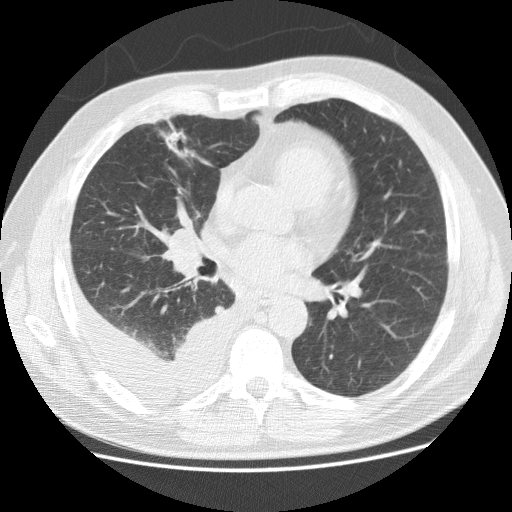
Axial slice from a low-dose chest CT screening exam; baseline screening round; lung window (W 1500 / L -600 HU); 2.5 mm slice thickness; 120 kVp. Male, age 65 years at enrolment. Current smoker at enrolment.
Expert-annotated lung lesion, bounding box (x1, y1, x2, y2) in pixels: (149, 121, 215, 174). The exam's reader record, not a measurement of the box and not confirmed to be the same lesion: non-calcified nodule or mass ≥4 mm, right middle lobe, 22 × 15 mm, spiculated (stellate) margins, mixed attenuation. Official screen result: positive, change unspecified: nodule(s) >= 4 mm or enlarging nodule(s), mass(es), or other non-specific abnormalities suspicious for lung cancer. Later outcome: lung cancer diagnosed 4 days after this screen — adenocarcinoma, NOS, right middle lobe, stage IV (AJCC 6th edition), 20 mm at pathology.